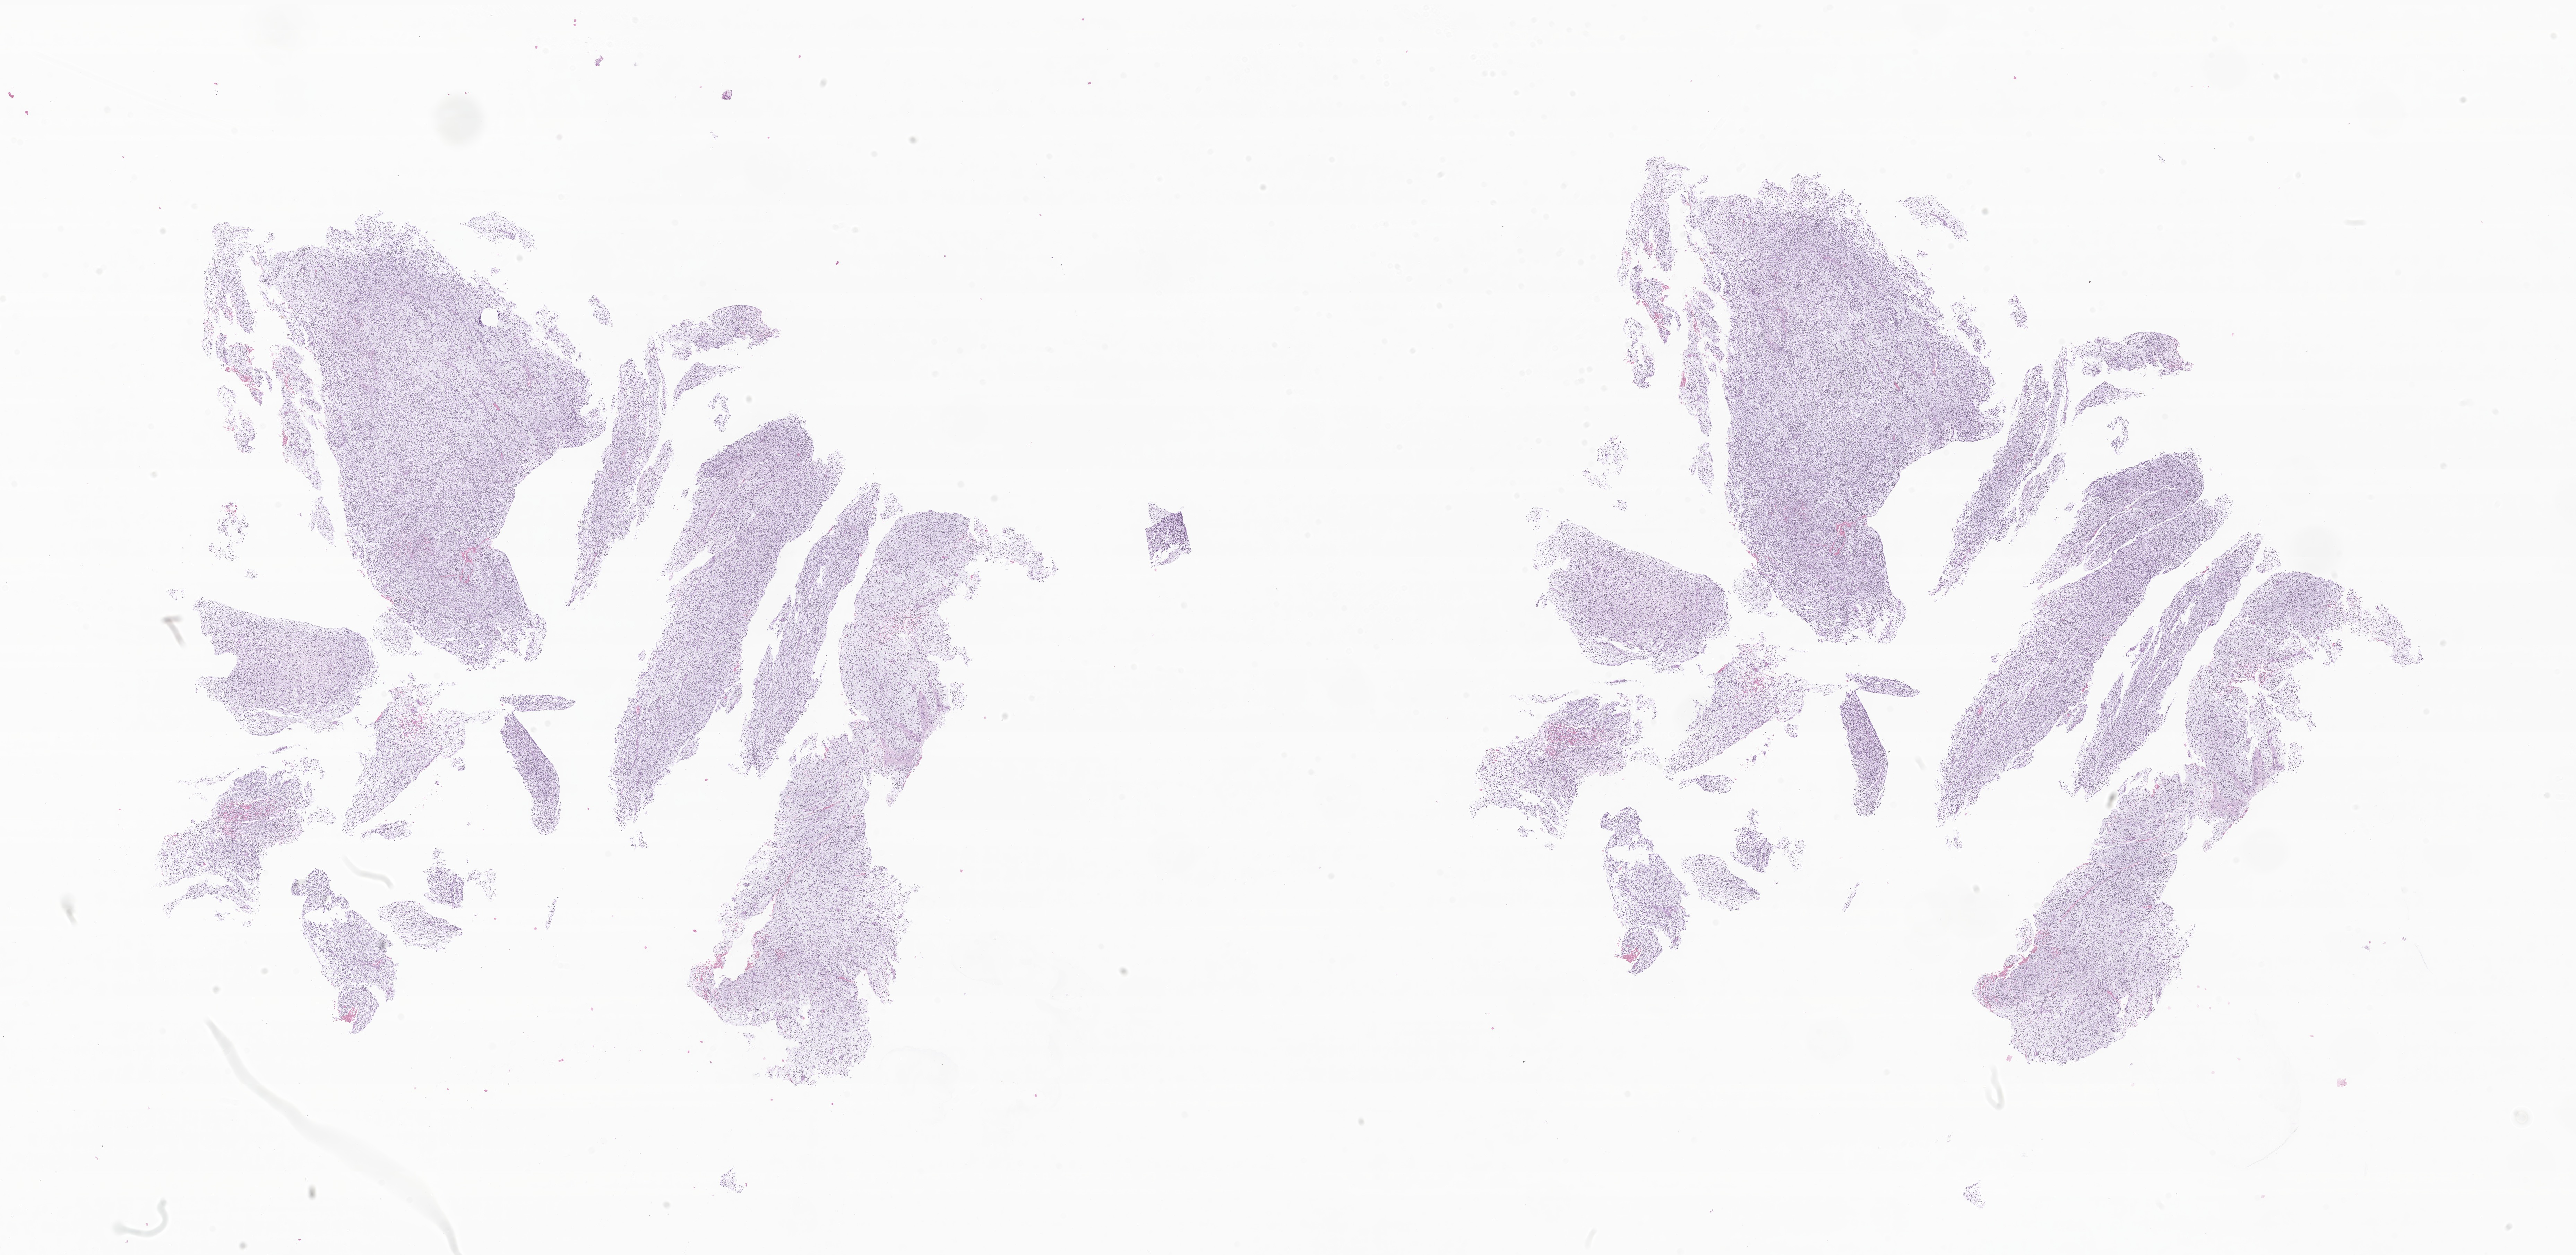
Whole-slide image, haematoxylin and eosin stain of tumor tissue from the orbit, shown as a low-resolution overview of the whole scanned area (about 31.3 x 15.3 mm), FFPE section. Female patient, age 95 months (7 years 11 months).
Recorded diagnosis: Embryonal rhabdomyosarcoma, NOS.